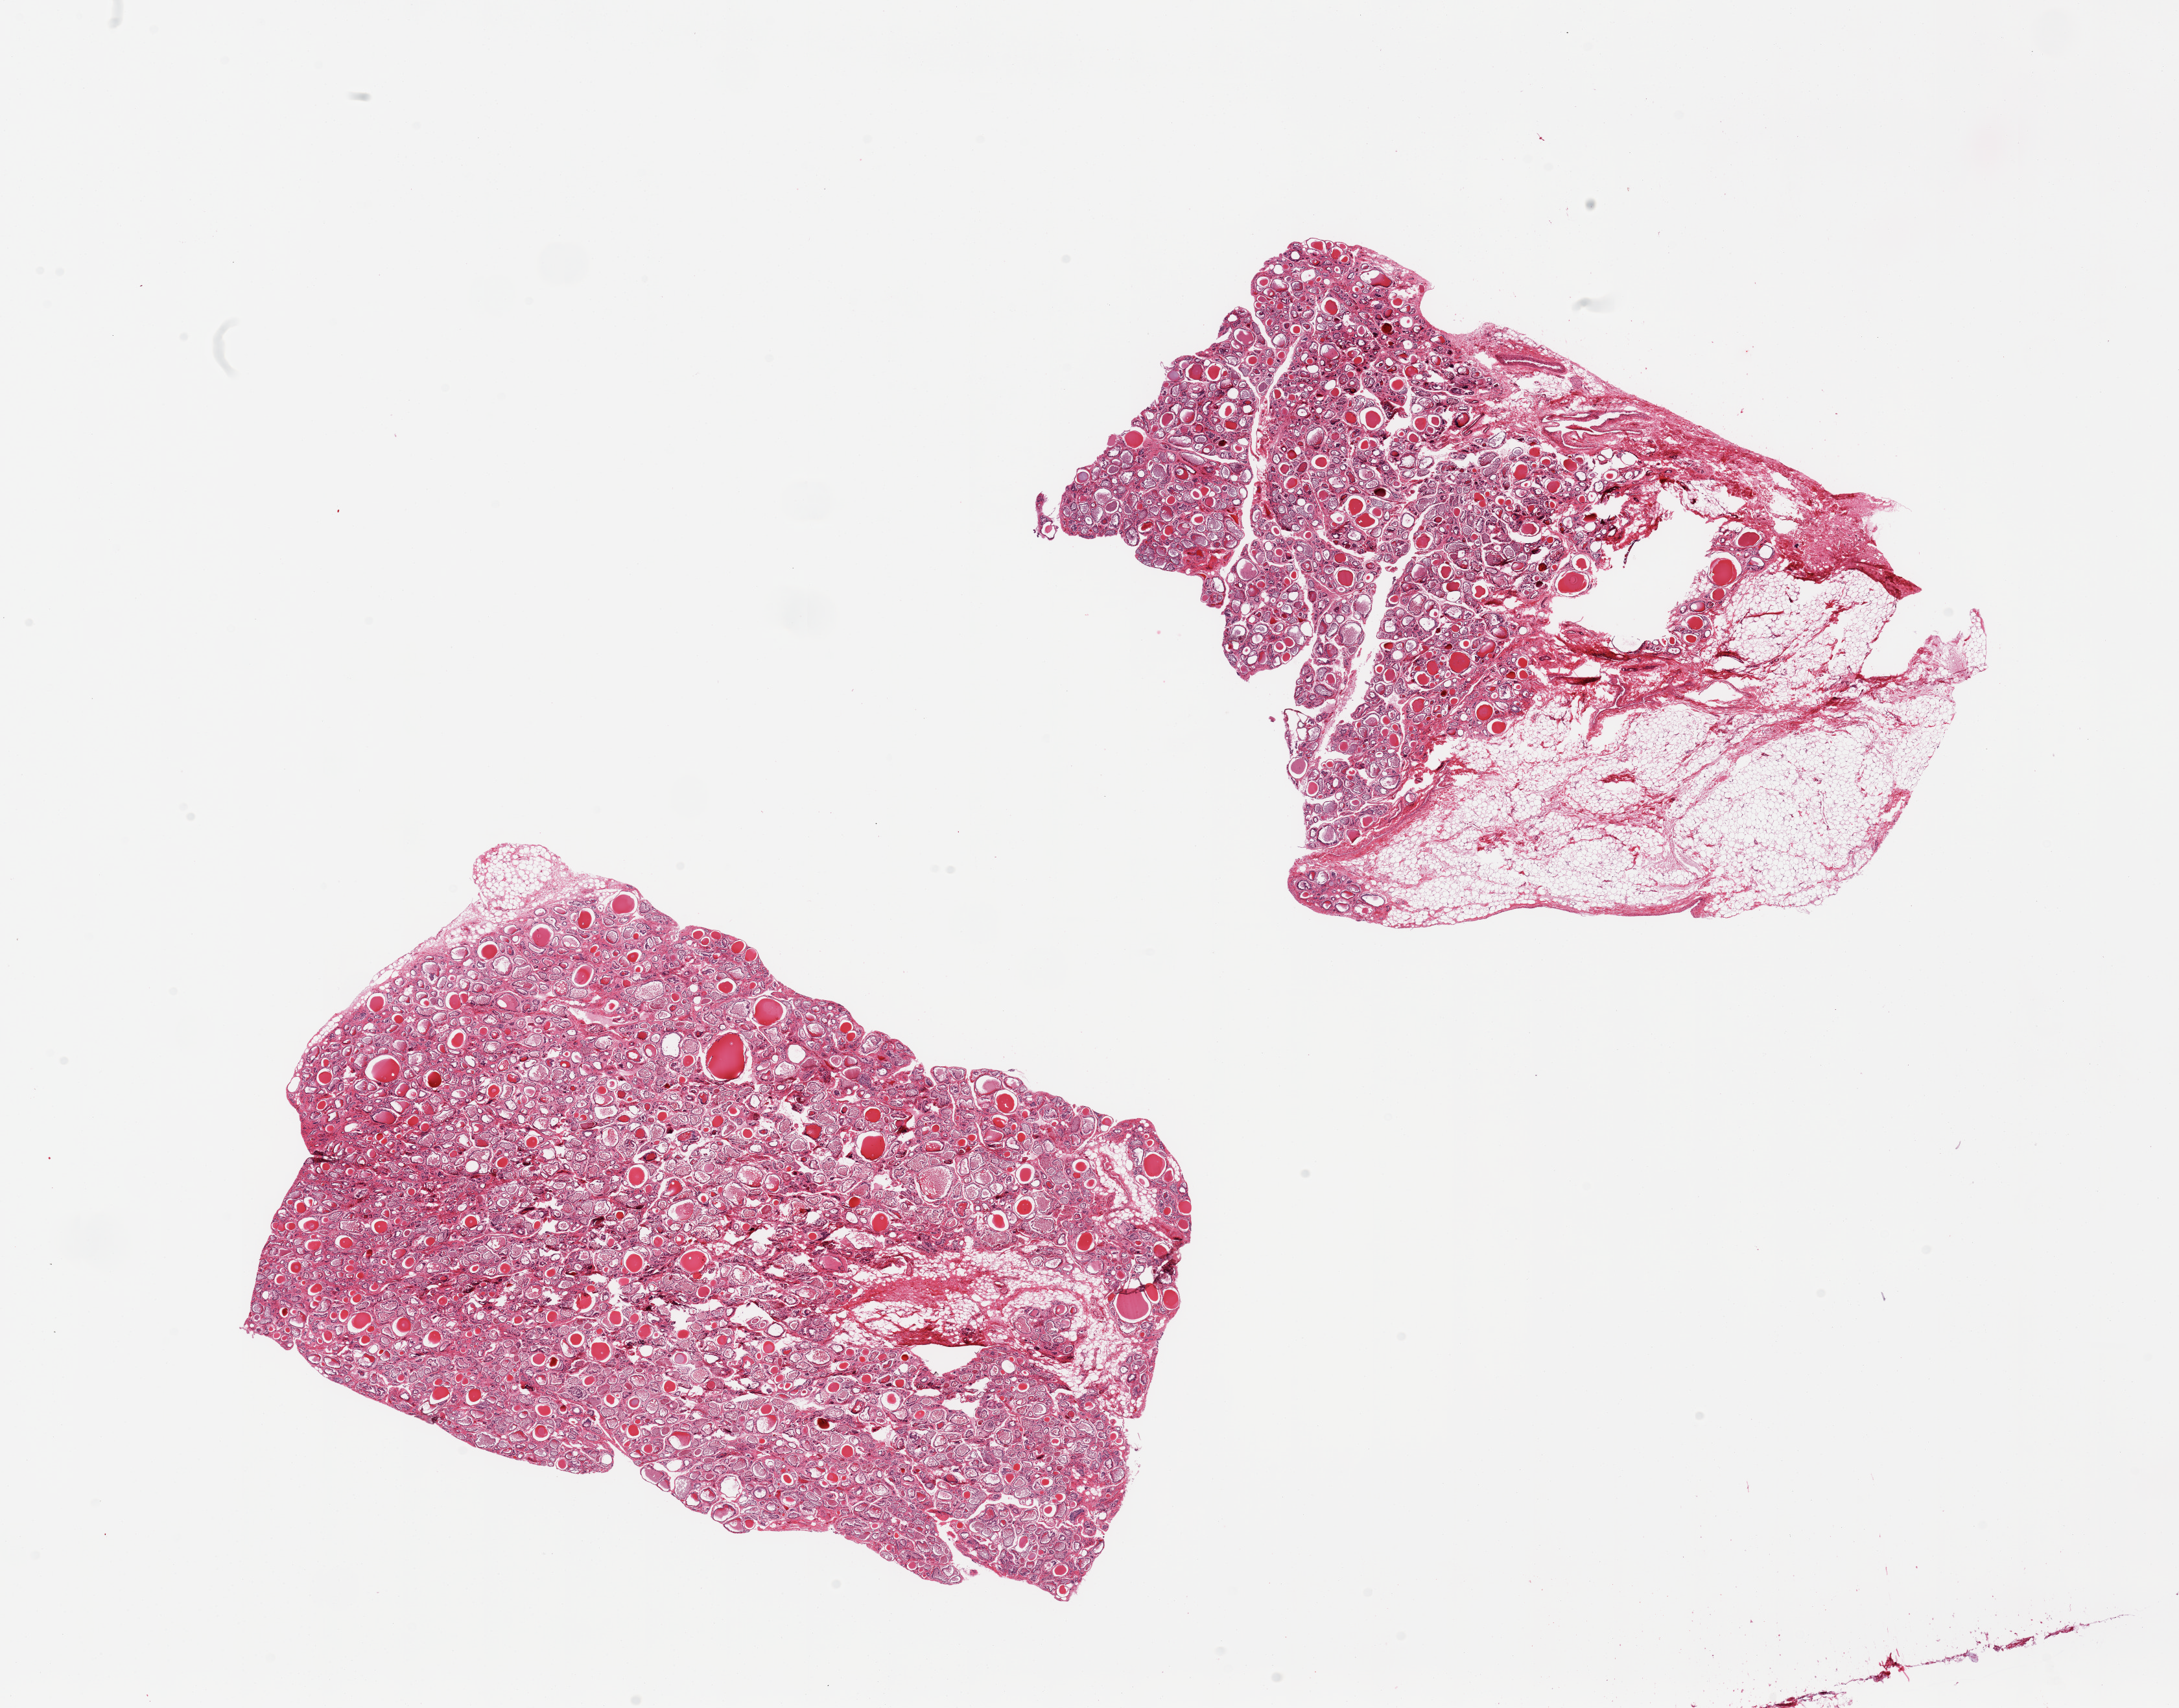
Whole-slide image, haematoxylin and eosin stain — low-resolution overview of the scanned area, about 26.6 x 20.8 mm (from a 20x scan). PAXgene-fixed paraffin-embedded (PFPE) section. Target tissue: thyroid. Tissue donor sample.
Review note (as recorded): 2 pieces, unusually pronounced autolysis, ~20% total fat (~3mm nubbin adherent fat on one aliquot).